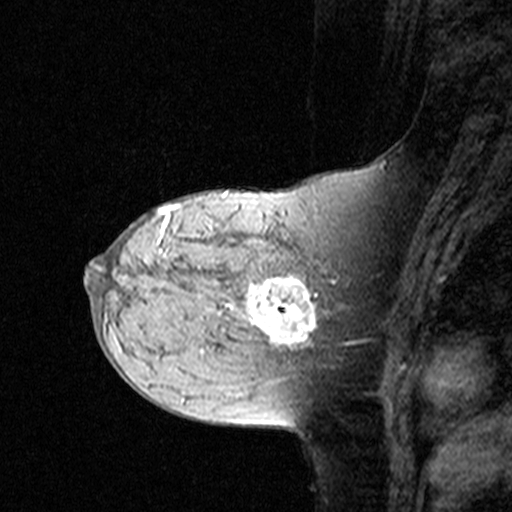
Breast MRI (dynamic contrast-enhanced), one sagittal slice. Slice 16 of 44 in the series (ordered by position). Dynamic contrast-enhanced study with each time point stored as its own series, time point 2 of 3 at this slice position (early post-contrast, ordered by acquisition time). 1.5 T. TE 4.5 ms, TR 11 ms. 3 mm slice thickness. 512 × 512 image matrix. Female patient, age 44 years. Case-level facts recorded for this patient, not image findings: setting: breast cancer imaged before/during neoadjuvant chemotherapy; receptor status: triple-negative.
Outlined on this slice (semi-automatically segmented with operator editing):
- analysis volume of interest (the breast-tissue region the enhancement analysis was run in; not a lesion): bounding box (x1, y1, x2, y2) in pixels: (142, 208, 349, 363)
- tumour enhancement mask (voxels above the 90 % enhancement threshold inside the analysis volume of interest): (226, 277, 349, 349)